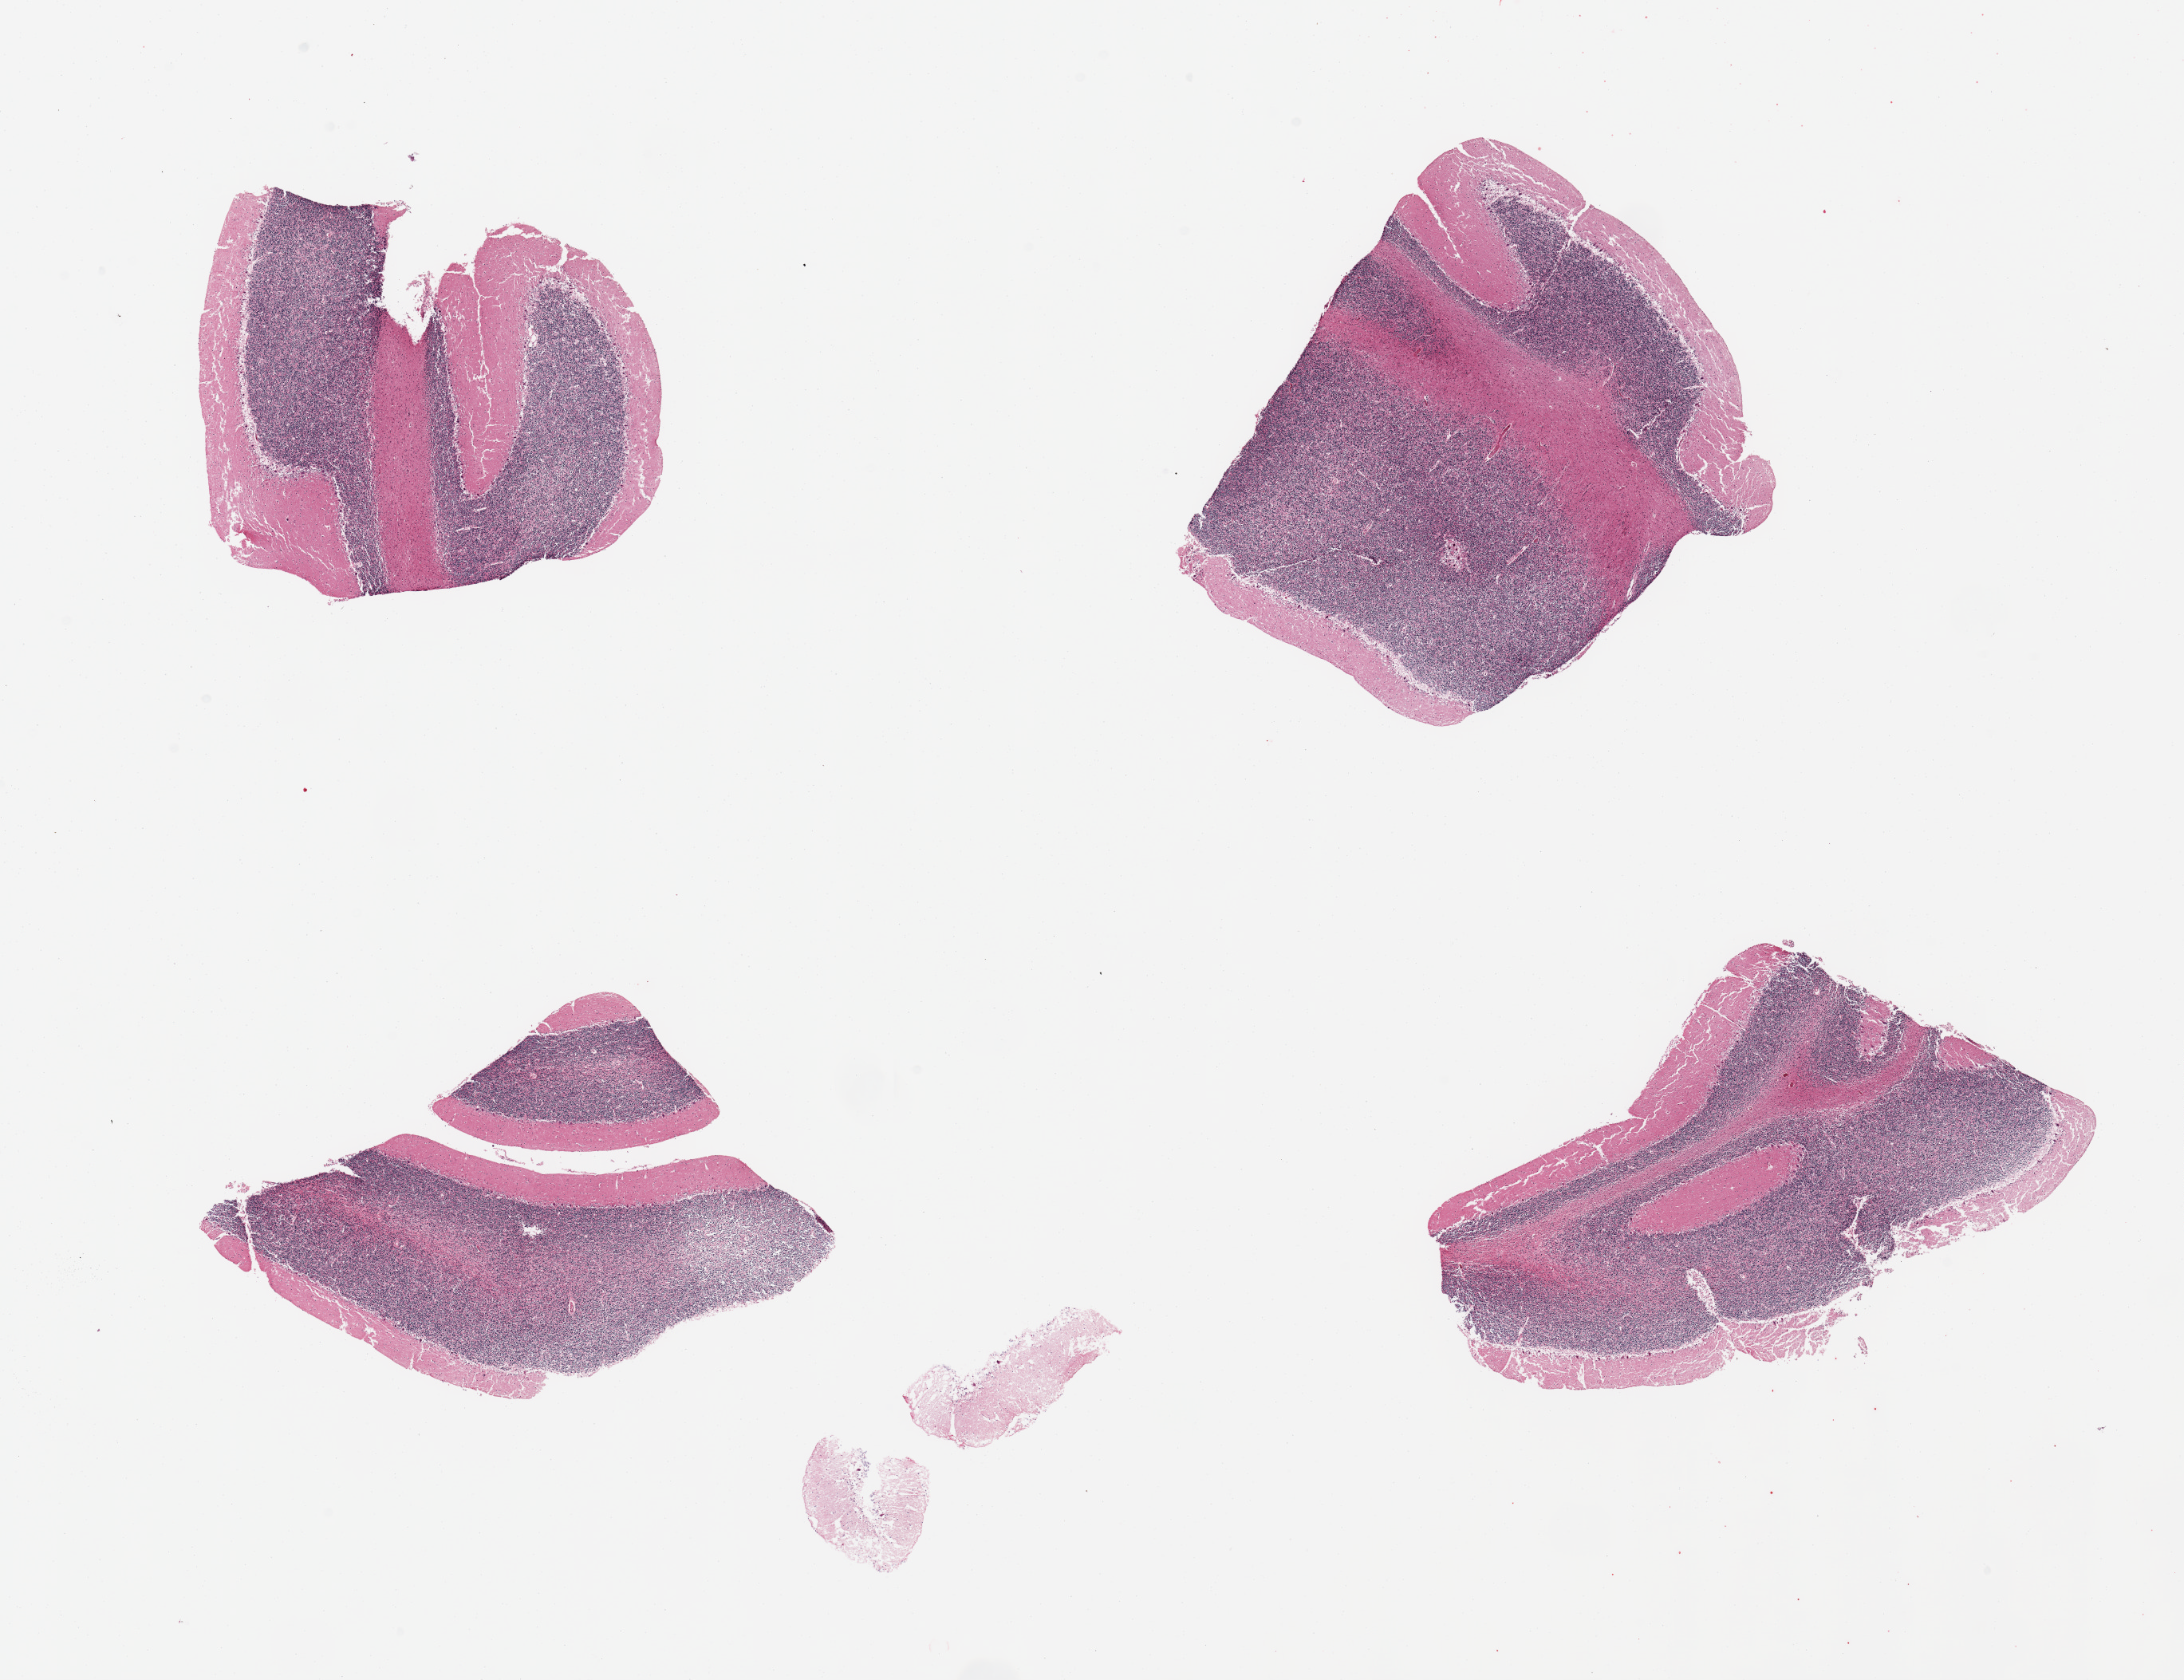
Whole-slide image, hematoxylin and eosin (H&E) stain, brightfield, whole scanned area (about 21.7 x 16.7 mm, slide scanned at 20x) shown as a low-resolution overview, PAXgene-fixed paraffin-embedded (PFPE) section, sampled site (target tissue): cerebellum, tissue donor sample.
Pathologist's review note for this sample: 4 pieces, no abnormalities.